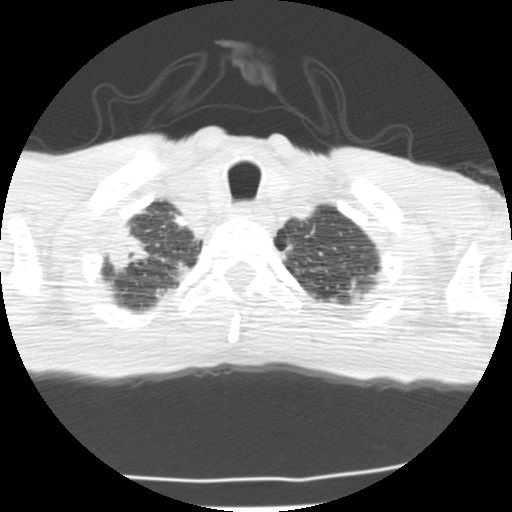
Low-dose screening chest CT, one axial slice; position 193 of 214 along the scan axis; reconstruction kernel STANDARD; 120 kVp; lung window (W 1500 / L -600 HU); 2.5 mm slice thickness; 512 × 512 image matrix, field of view 283 × 283 mm.
Annotated regions visible in this slice (manually delineated by an expert):
- lesion 1 (tumor, upper lobe of right lung): box from (x=110, y=226) to (x=149, y=273) px